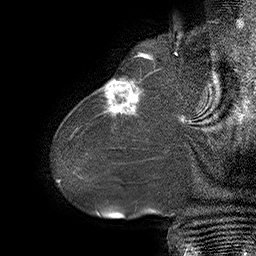
Breast MRI (dynamic contrast-enhanced), one sagittal slice. Position 10 of 55 along the scan axis. Dynamic contrast-enhanced series, time point 2 of 6 at this slice position (early post-contrast). 1.5 T. TE 4.5 ms, TR 32.4 ms. 3 mm slice thickness. 256 × 256 image matrix, field of view 180 × 180 mm. Female patient. Case-level facts recorded for this patient, not image findings: setting: breast cancer imaged before/during neoadjuvant chemotherapy; receptor status: HER2-positive.
Annotated regions visible in this slice (semi-automatic segmentation, software-assisted and operator-edited):
- analysis volume of interest (the breast-tissue region the enhancement analysis was run in; not a lesion): bounding box [x1, y1, x2, y2] px = [80, 64, 163, 134]
- tumour enhancement mask (voxels above the 100 % enhancement threshold inside the analysis volume of interest): [102, 79, 141, 116]